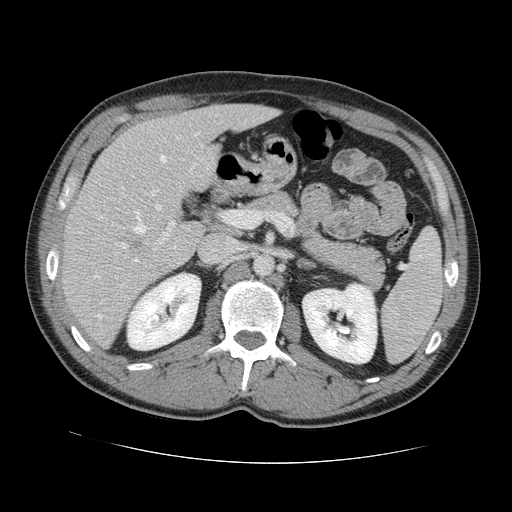
Contrast-enhanced abdominal CT, one axial slice; position 75 of 131 along the scan axis; 120 kVp; intravenous contrast given; soft-tissue window (W 400 / L 40 HU); 2.5 mm slice thickness; 512 × 512 image matrix, field of view 380 × 380 mm. Male patient, age 40 years. Case-level facts recorded for this patient, not image findings: diagnosis: colorectal cancer liver metastases, imaged before liver resection; multiple liver metastases: yes.
Outlined on this slice (expert manual segmentation):
- hepatic veins: box from (x=94, y=155) to (x=167, y=318) px
- liver: (x=65, y=105)–(x=274, y=345)
- planned liver remnant (the part of the liver to remain after resection): (x=106, y=105)–(x=274, y=196)
- portal vein (with intrahepatic branches): (x=133, y=189)–(x=234, y=263)
- liver metastasis: (x=128, y=235)–(x=147, y=249)